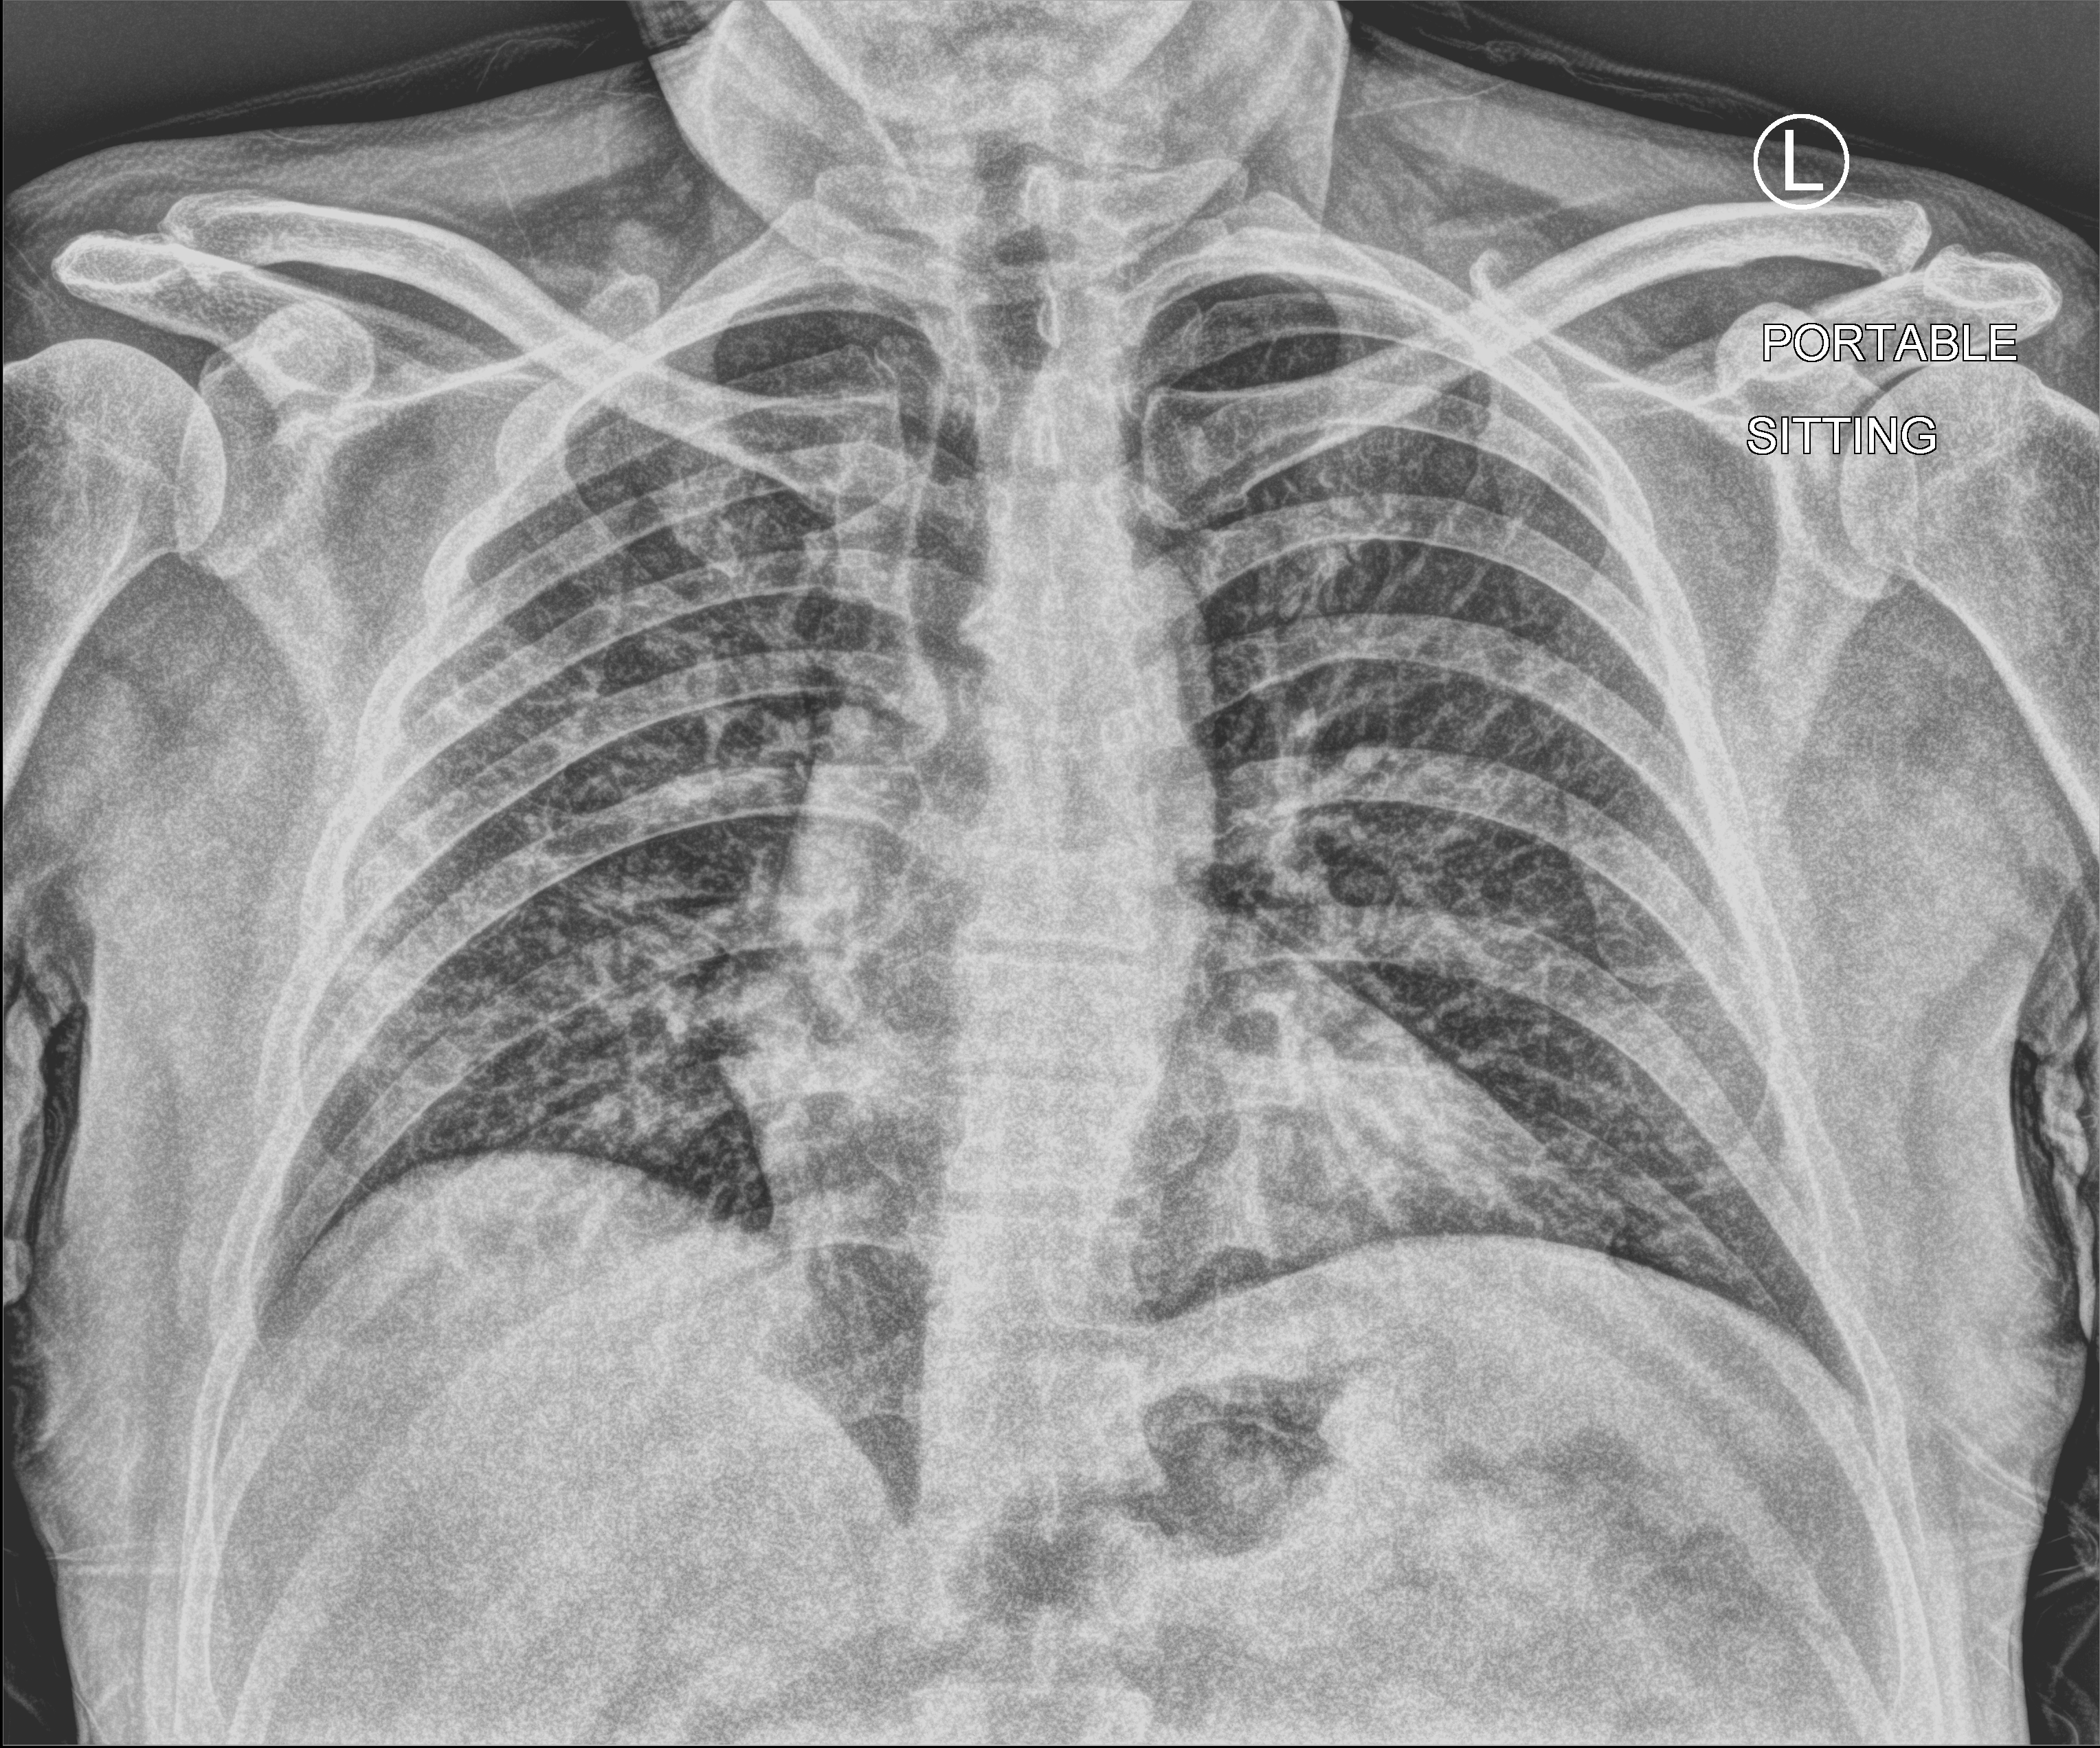
Bedside chest radiograph (computed radiography). Patient hospitalised with COVID-19; male, aged 18–59 years.
From the hospital-stay record, not from the radiograph (when in the stay this image was taken is not recorded): mechanically ventilated during this hospital stay: no; admitted to intensive care during this hospital stay: no.